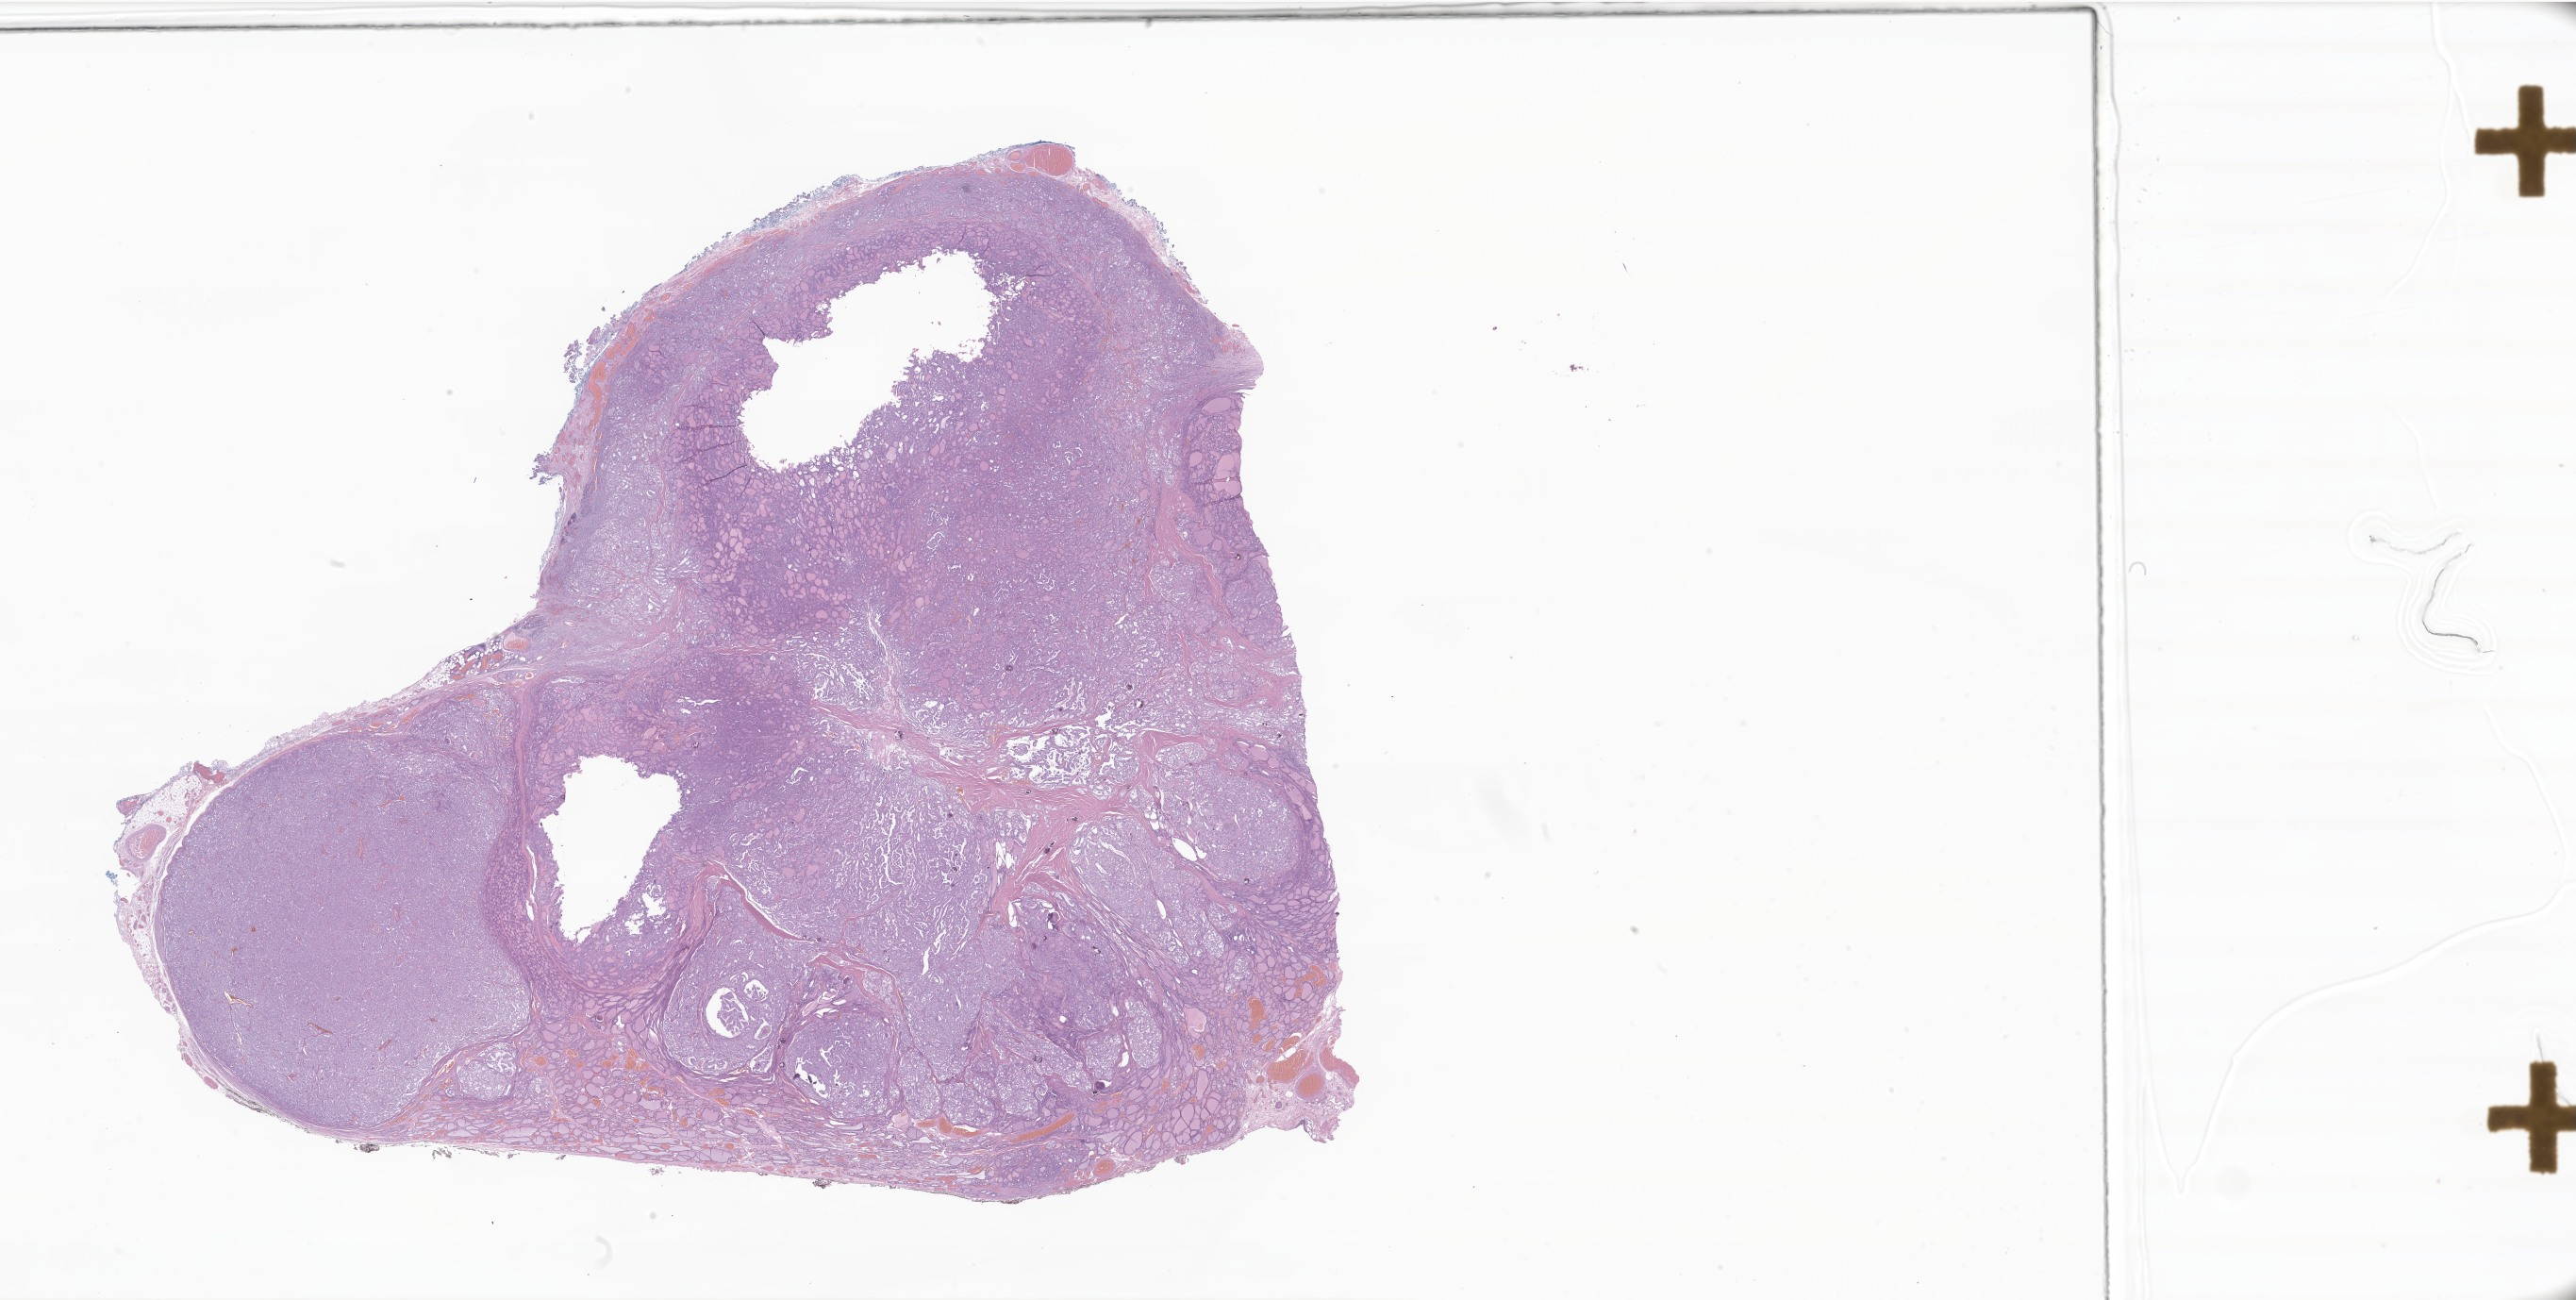
Whole-slide image, hematoxylin and eosin (H&E) stain of tumor tissue from the thyroid — a low-resolution overview of the entire scanned area, about 46.0 x 23.2 mm. Formalin-fixed, paraffin-embedded (FFPE) tissue. Patient: male, age 195 months (16 years 3 months).
Diagnosis (ICD-O-3 morphology term): Papillary carcinoma, NOS.